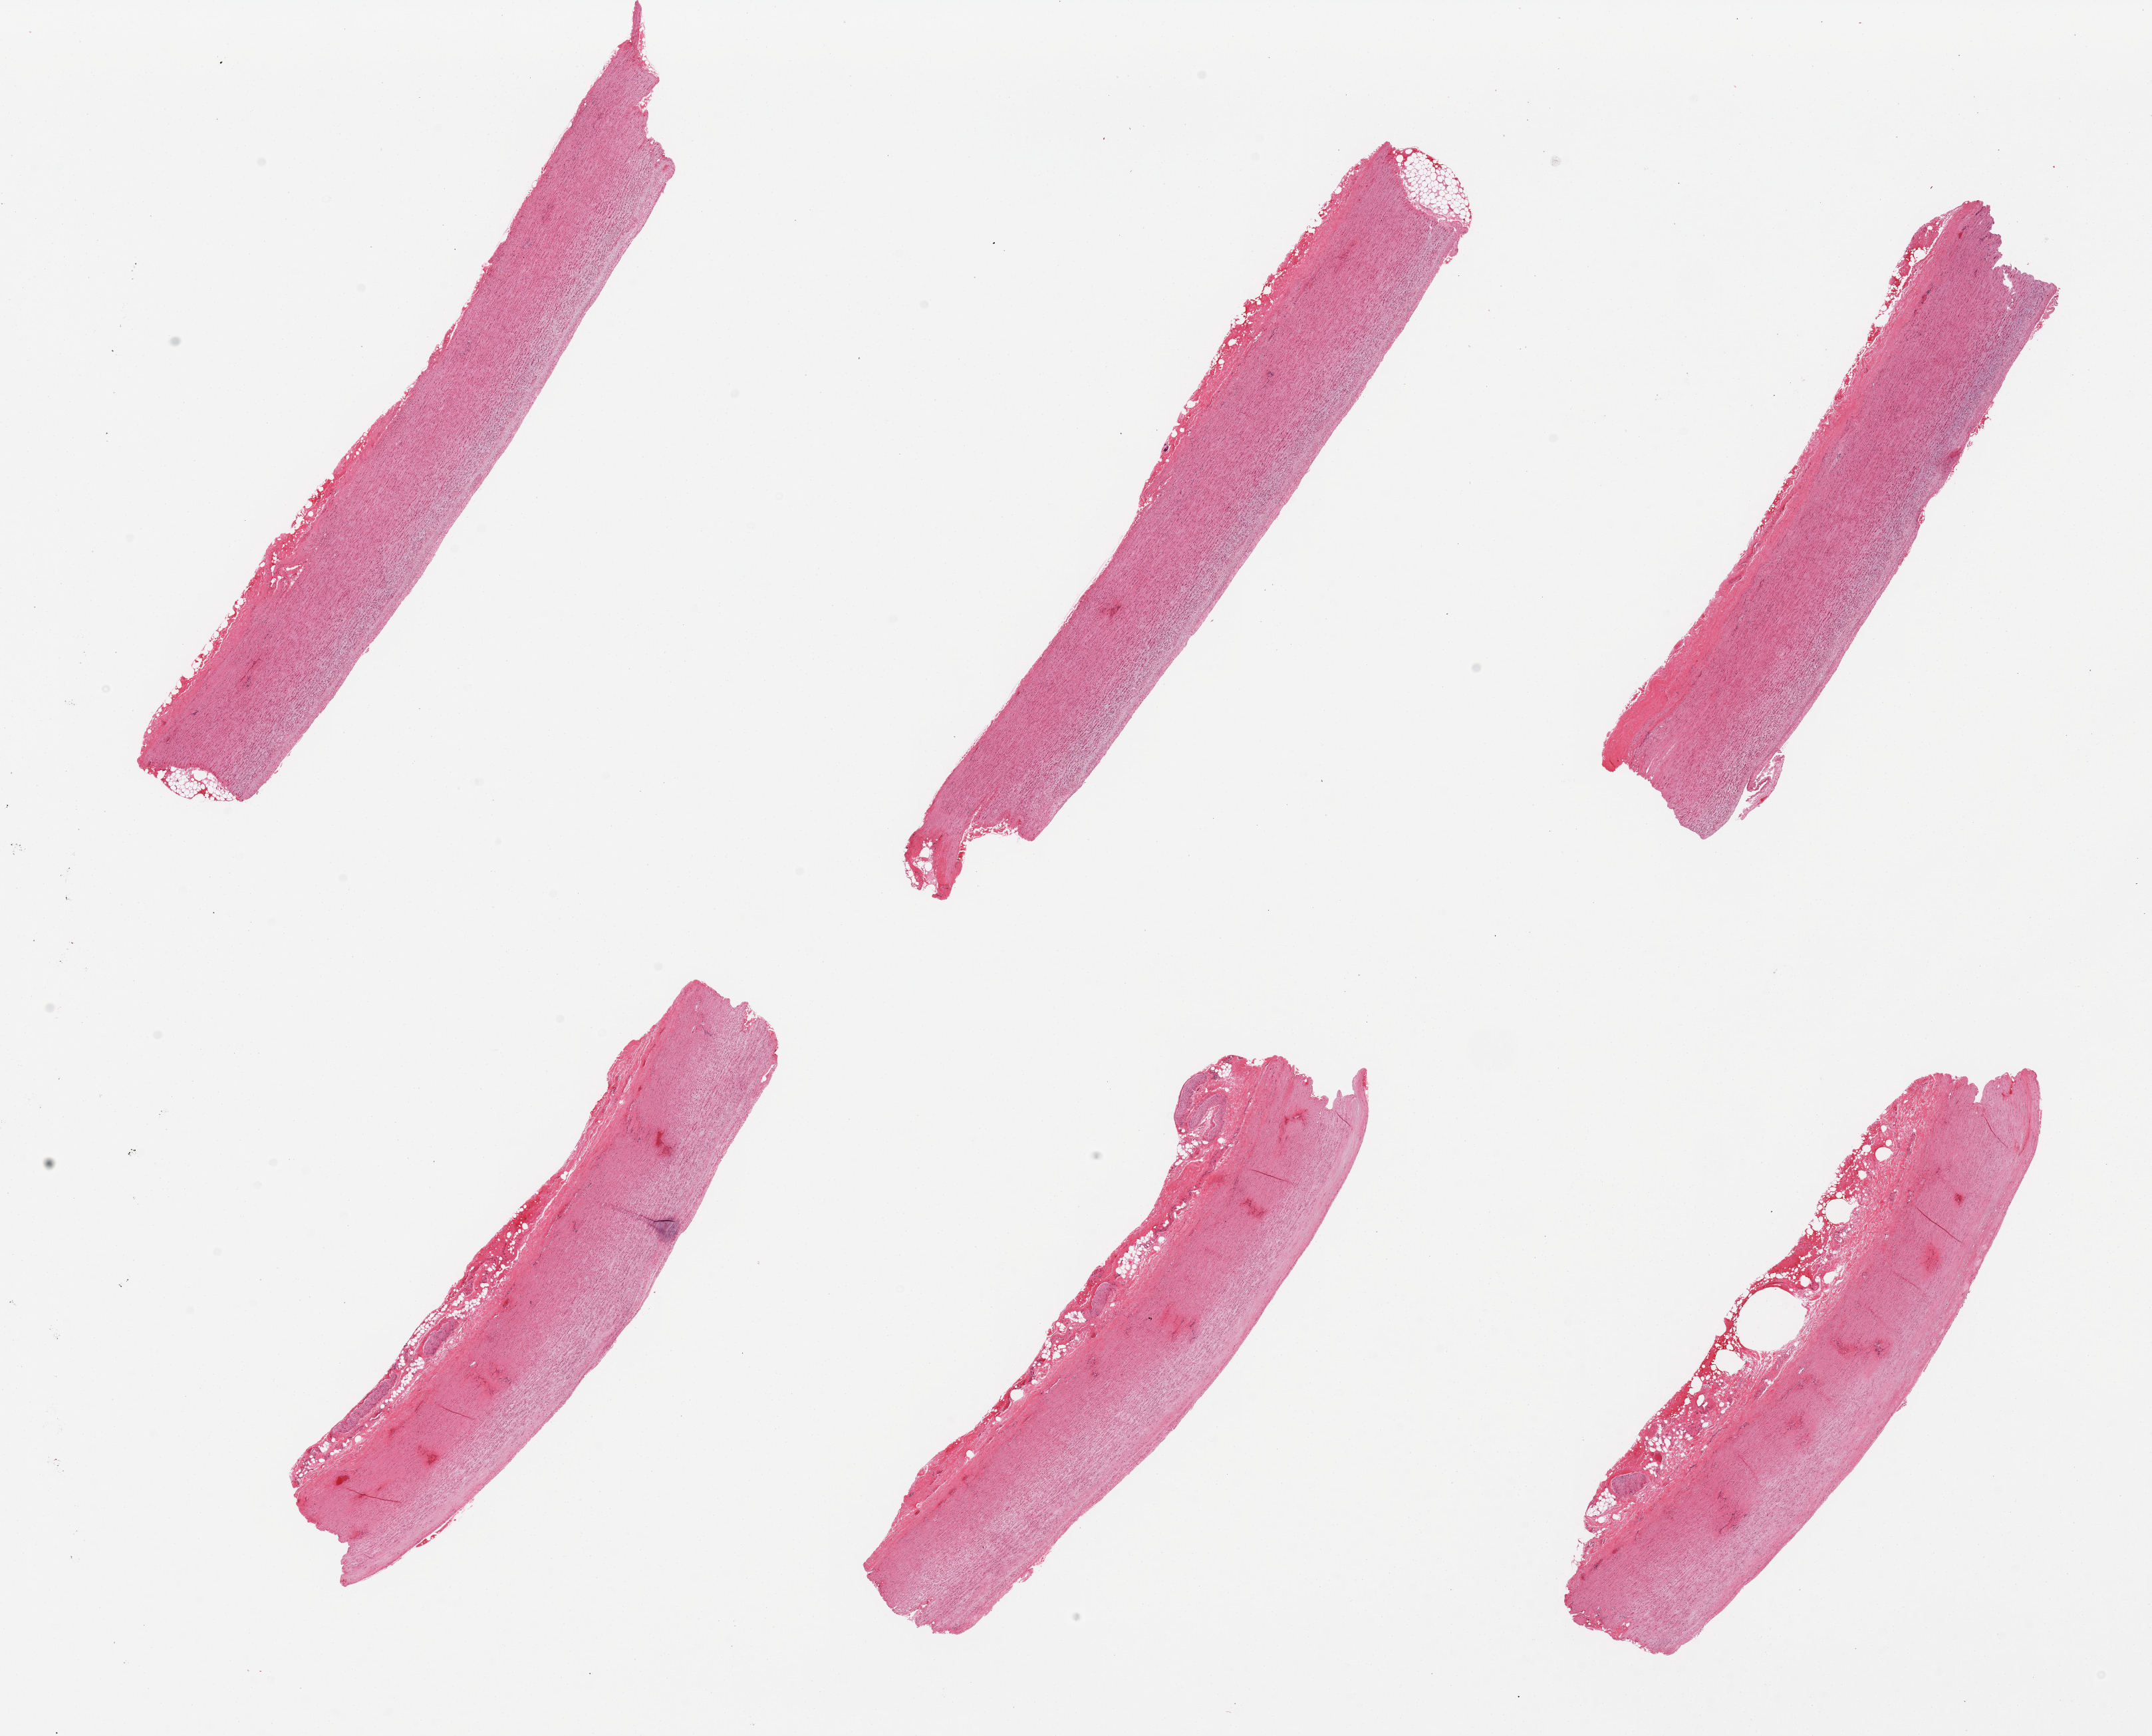
Whole-slide image, H&E stain, low-resolution overview of the scanned area, about 25.6 x 20.6 mm (slide scanned at 20x); PAXgene-fixed, paraffin-embedded tissue; target tissue: aorta; tissue donor sample. Male donor.
Review note (as recorded): 6 pieces, mild atherosclerosis, some attached adventitia.